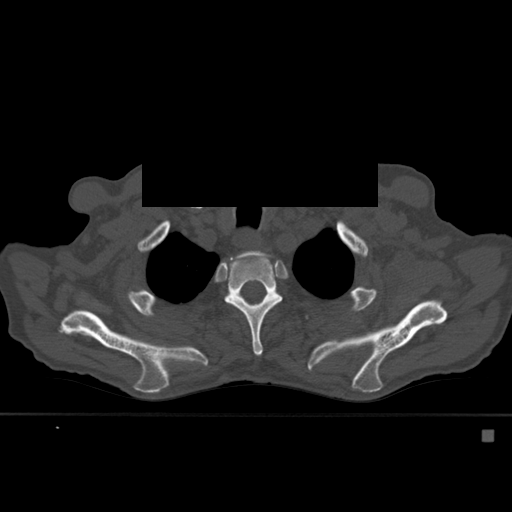
CT including the spine, one axial slice; slice 432 of 527 in the series (ordered by position); bone window (W 1800 / L 400 HU); 1.5 mm slice thickness; 512 × 512 image matrix, field of view 373 × 373 mm. Patient: male, 78 years. Case-level facts recorded for this patient, not image findings: primary cancer: prostate.
Annotated regions visible in this slice (semi-automatically segmented with operator editing):
- T2 vertebra: bounding box [x1, y1, x2, y2] px = [237, 251, 264, 259]
- T3 vertebra: [225, 253, 283, 356]
- T4 vertebra: [237, 293, 242, 297]